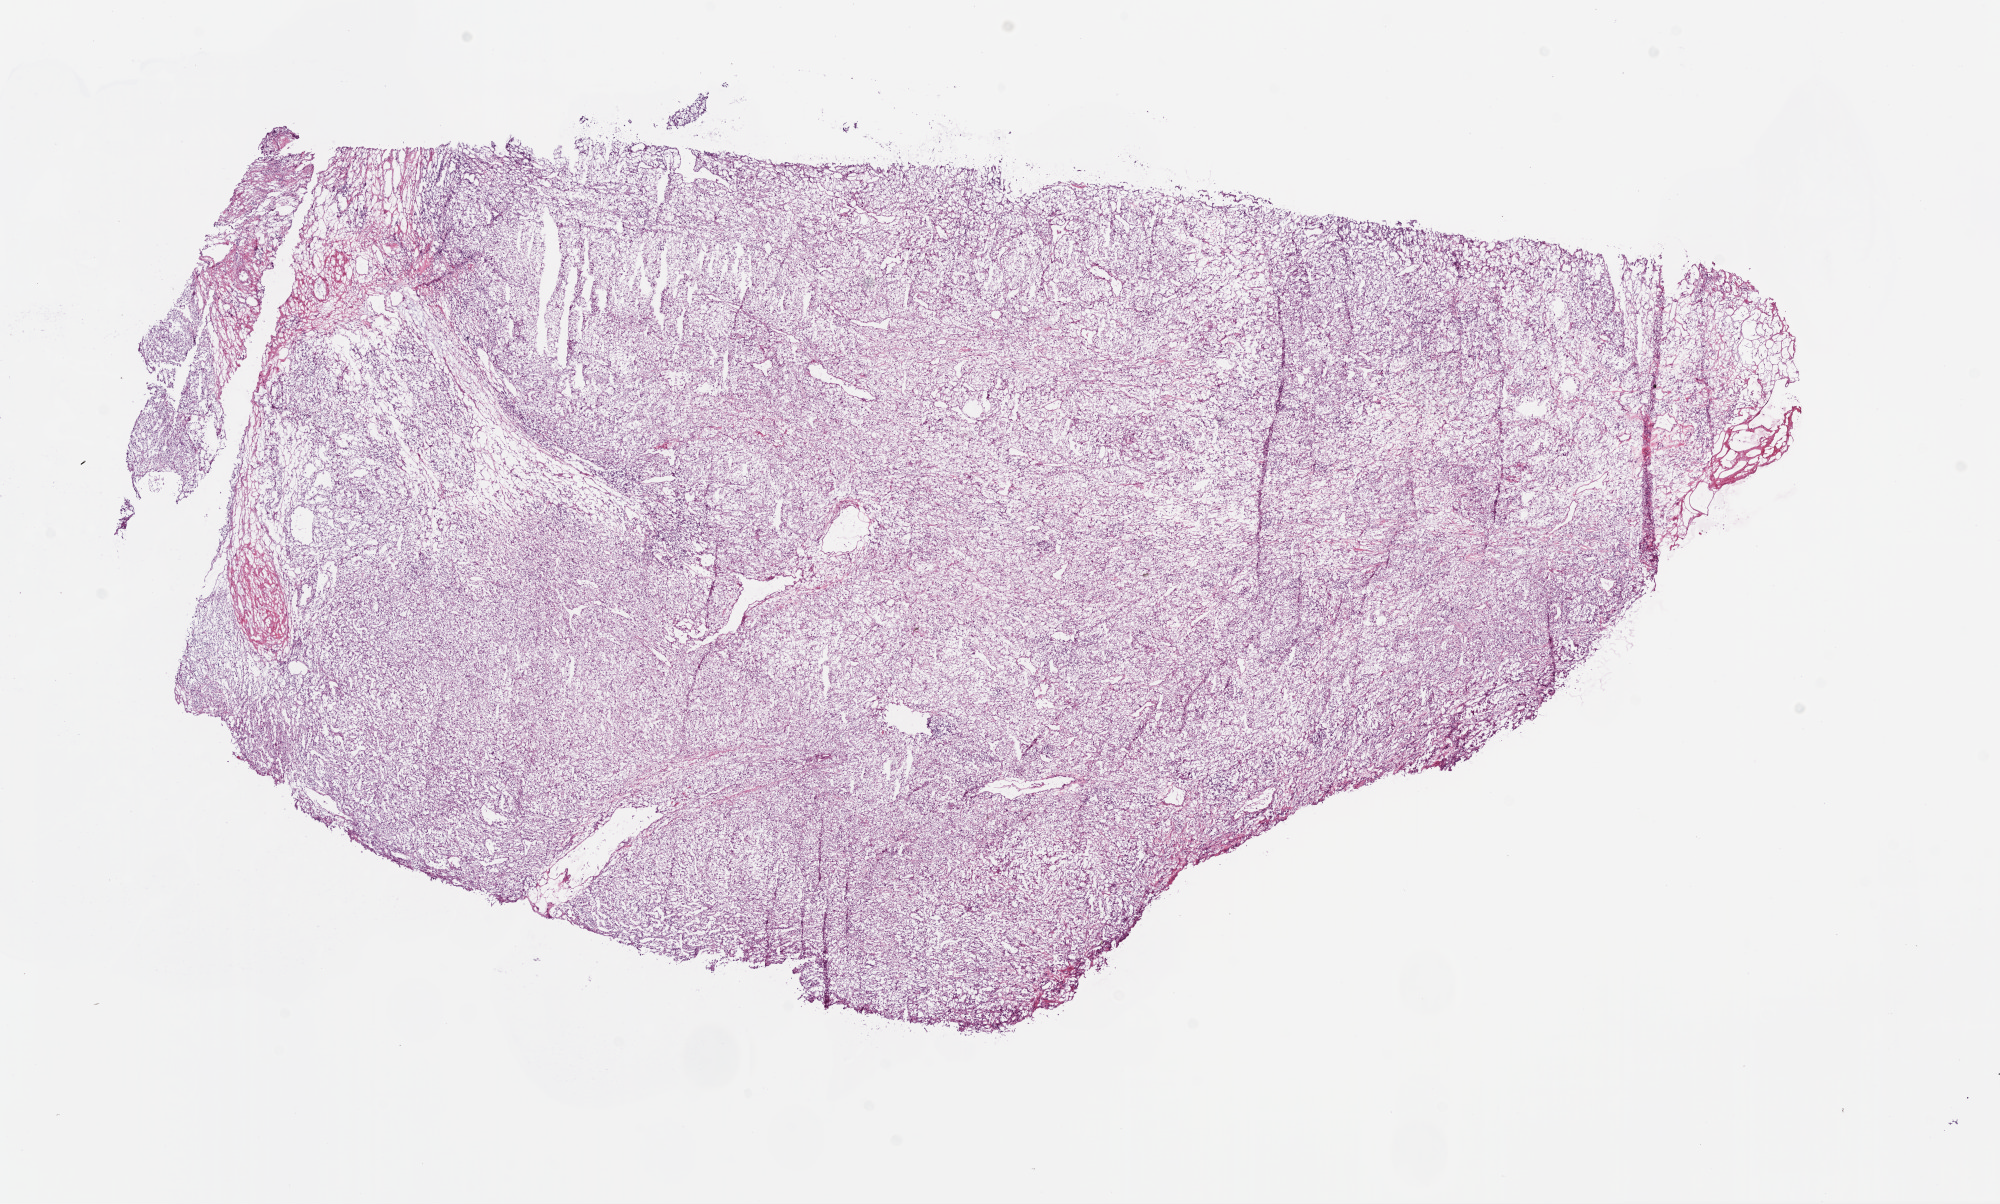
Digitized H&E tissue section (whole slide) — whole scanned area (about 16.0 x 9.7 mm) shown as a low-resolution overview; frozen section from the bottom of the tissue portion; primary tumour sample from the kidney. Female patient; age at initial diagnosis 79 years. Histologic grade: G2 (moderately differentiated). Composition of this section per pathologist review: tumour cells 90%, tumour nuclei 80%, normal cells 0%, stromal cells 10%, necrosis 0%.
* AJCC pathologic stage: III
* histologic diagnosis: Clear cell adenocarcinoma, NOS
* laterality: right